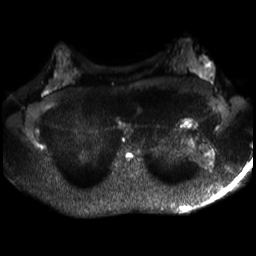
Breast MRI, one axial slice; slice 19 of 30 in the series (ordered by position); diffusion-weighted series; image 2 of 4 stored at this slice position (different b-values; order by instance number); 3 T; 4 mm slice thickness; 256 × 256 image matrix. Female patient.
Structures marked on this image (outlined manually by an expert reader):
- tumour on diffusion-weighted imaging: bounding box (x1, y1, x2, y2) in pixels: (202, 61, 213, 78)